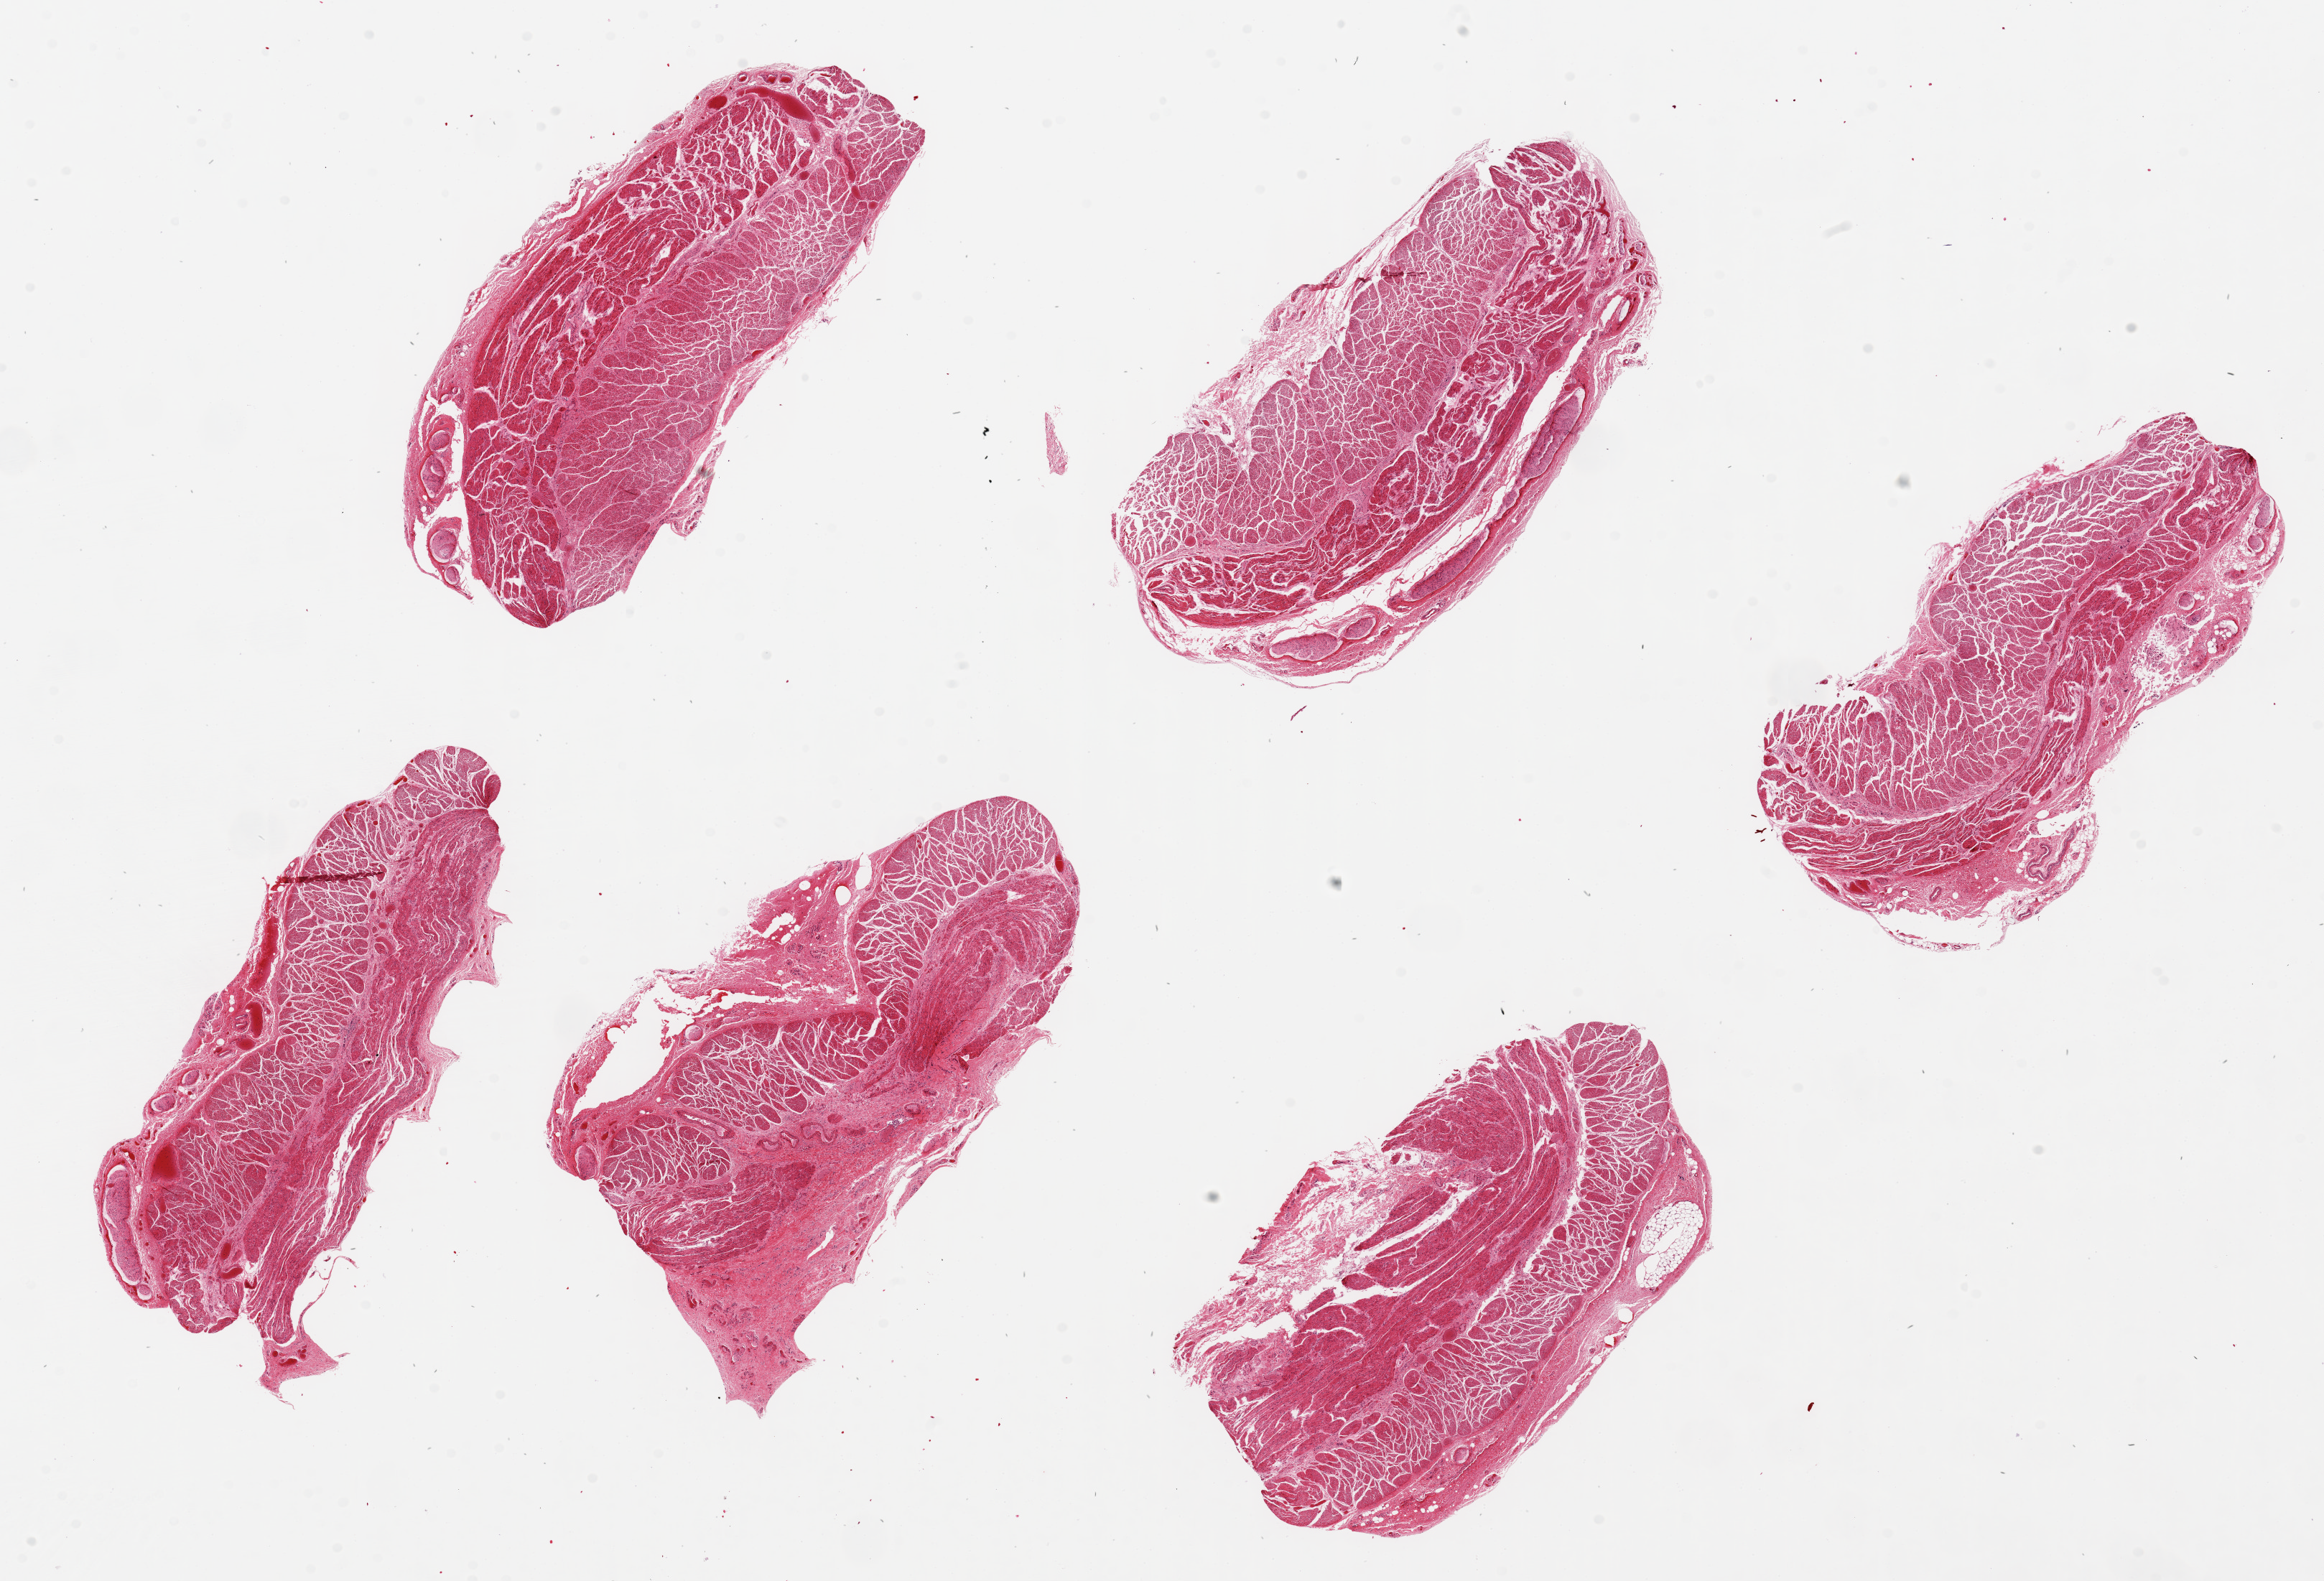
Haematoxylin and eosin whole-slide image, low-resolution overview of the scanned area, about 25.6 x 17.4 mm (from a 20x scan). PAXgene-fixed paraffin-embedded (PFPE) section. Sampled site (target tissue): esophageal muscle. Tissue donor sample. Donor sex: female.
- reviewer comment on this tissue sample: 6 pieces ~7x3mm, all muscularis, good specimens